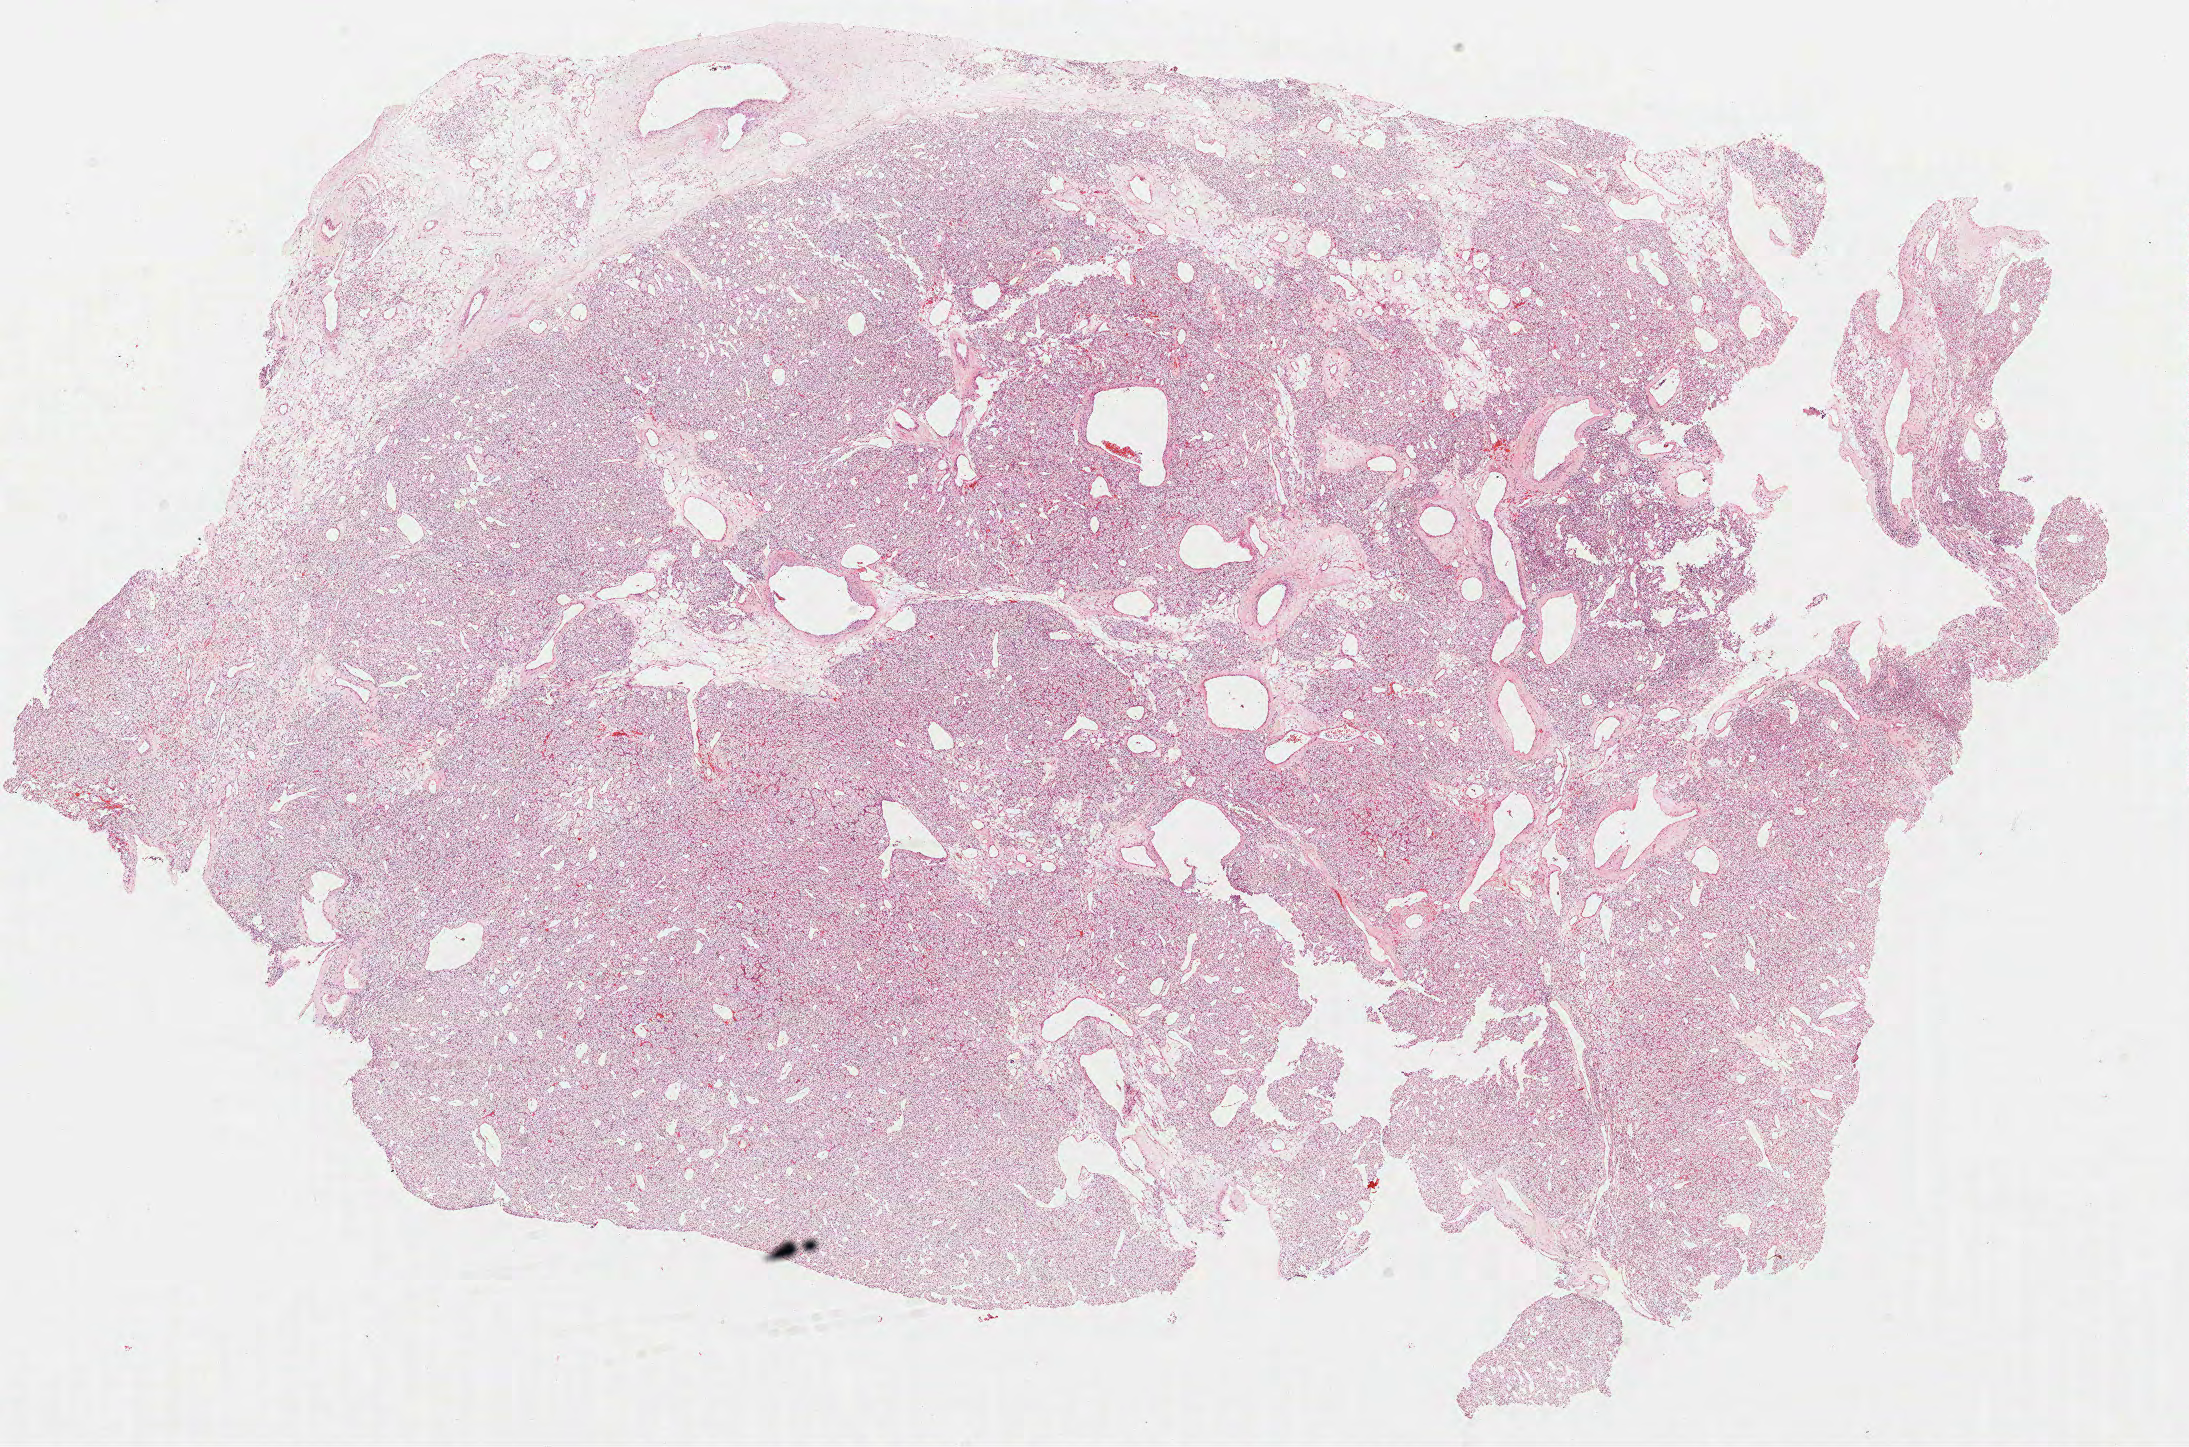
Digitized H&E tissue section (whole slide) — shown as a low-resolution overview of the whole scanned area (about 17.6 x 11.7 mm). Formalin-fixed paraffin-embedded (FFPE) diagnostic section. Kidney, primary tumour sample. Female patient; age at initial diagnosis 59 years. Histologic grade: G2 (moderately differentiated).
- histologic diagnosis: Clear cell adenocarcinoma, NOS
- AJCC pathologic stage: I